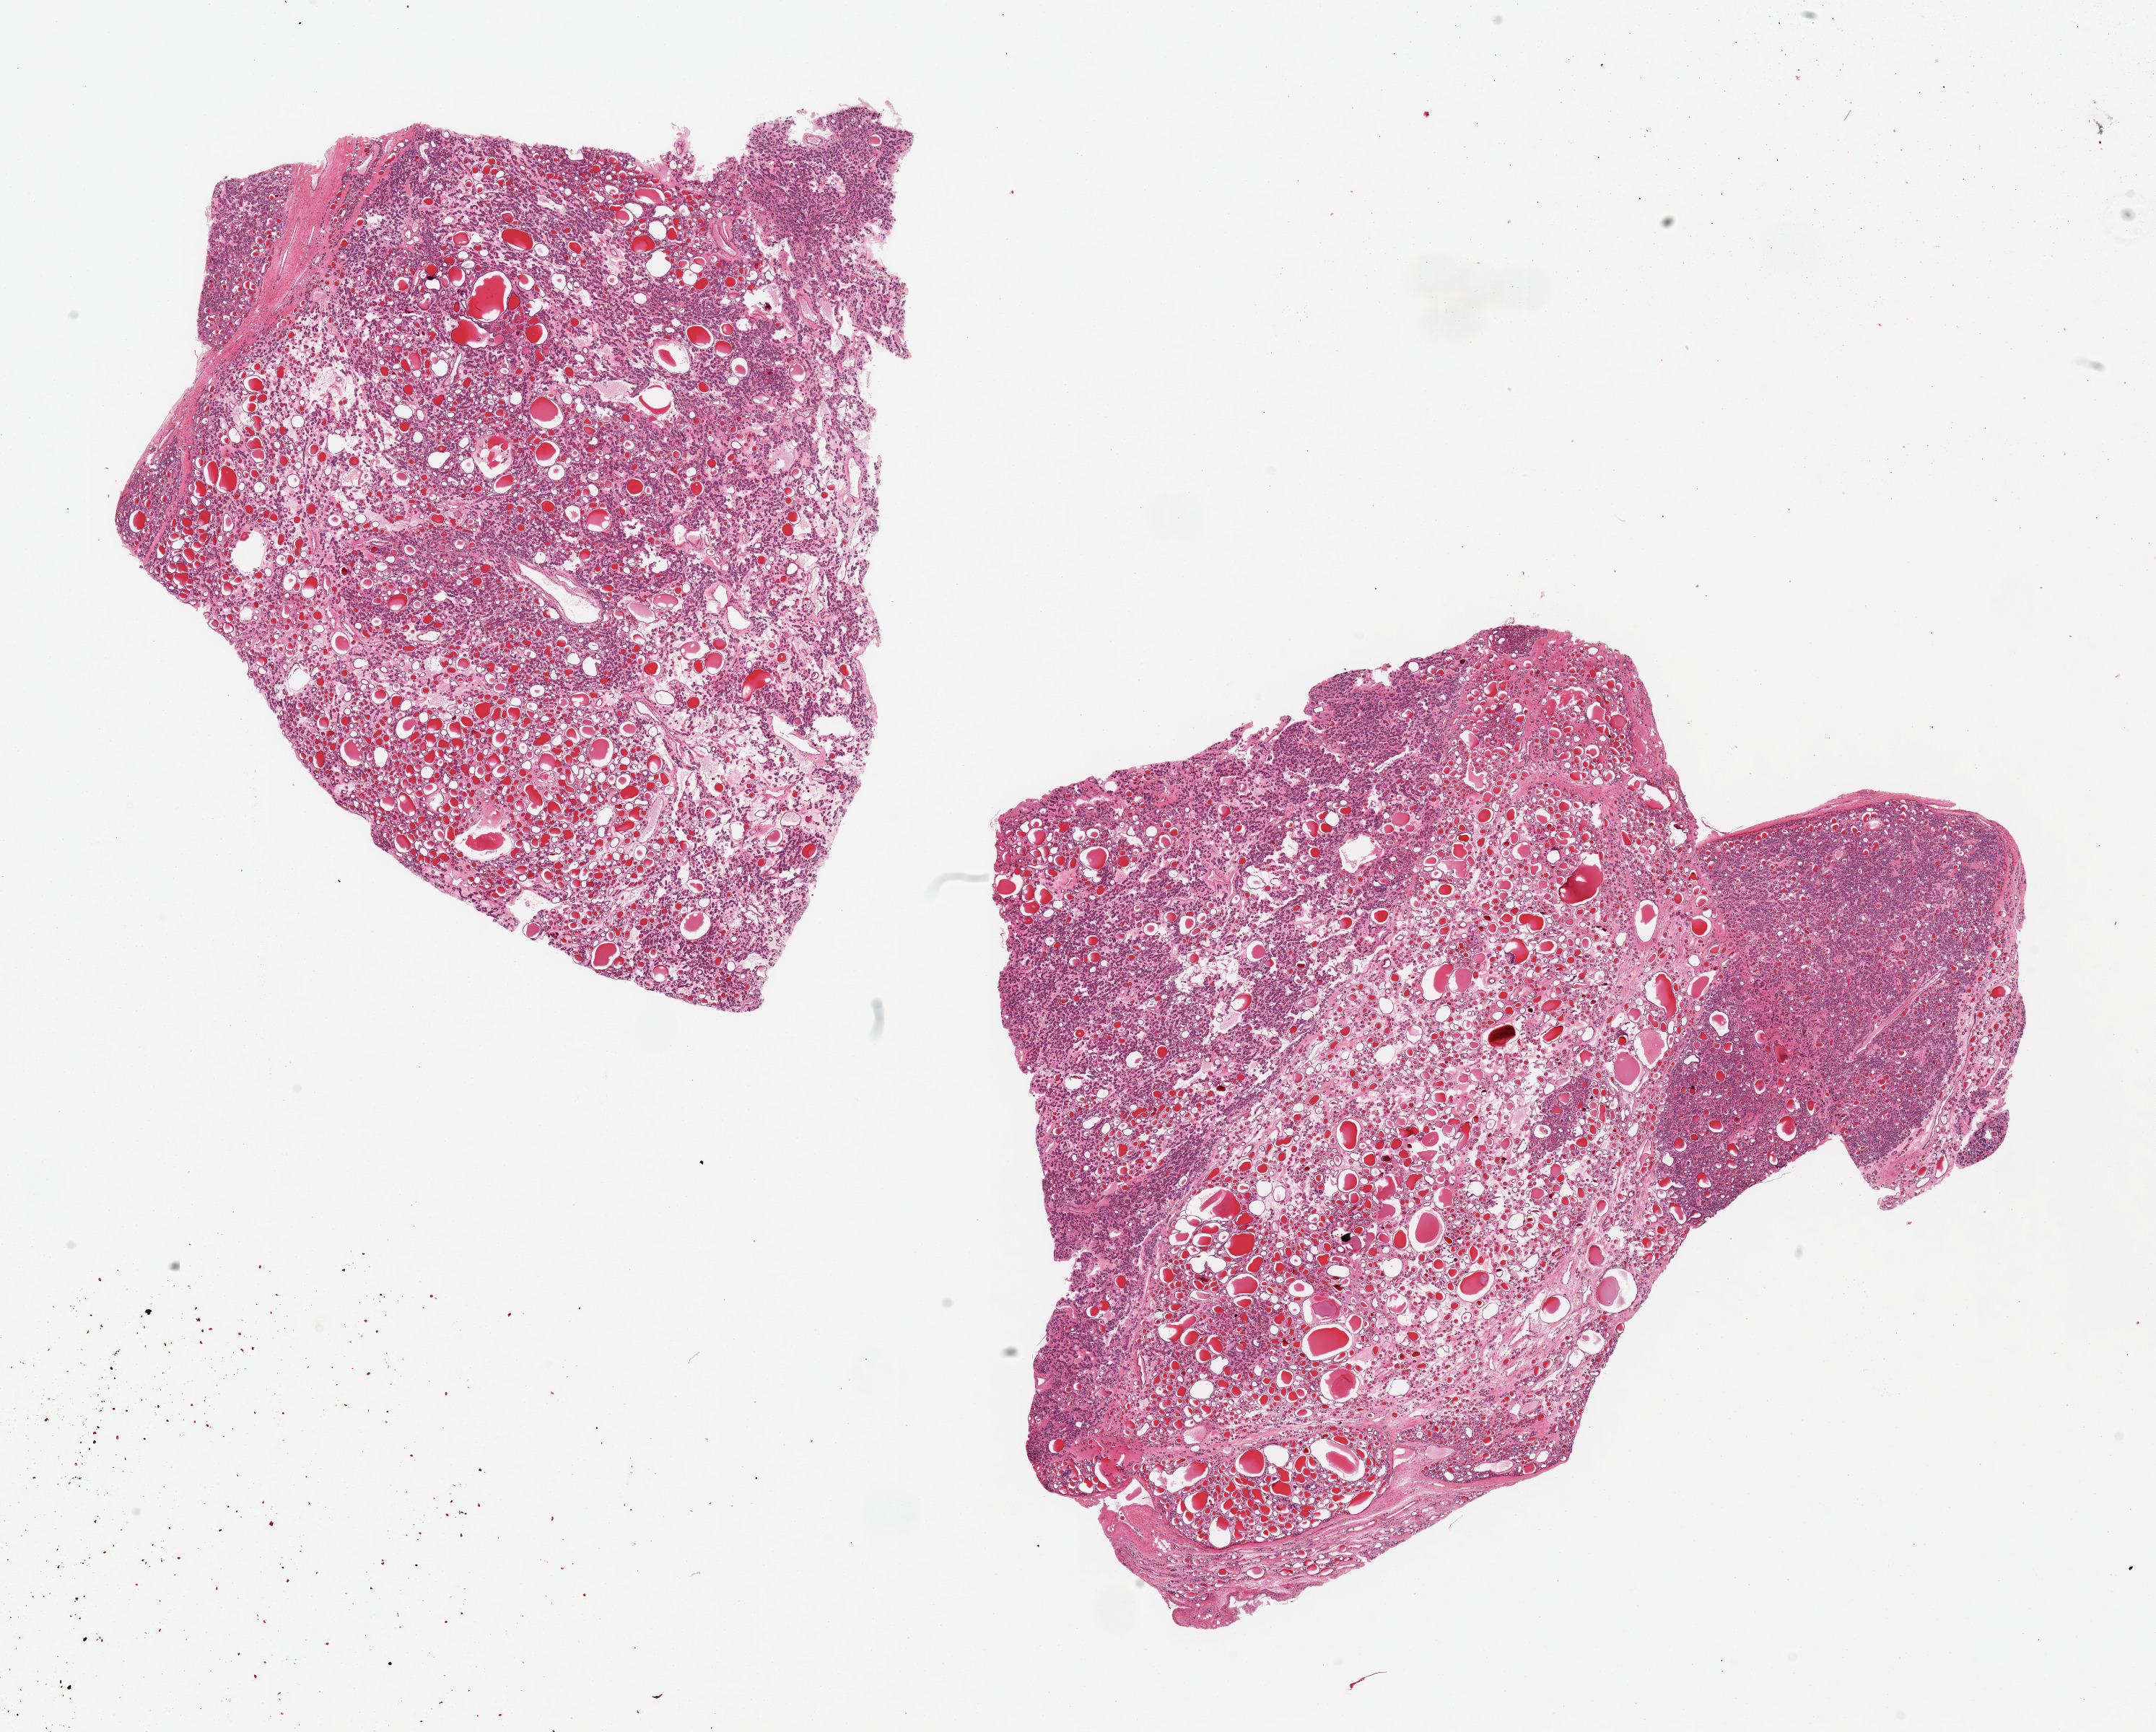
Whole-slide image, hematoxylin and eosin (H&E) stain — a low-resolution overview of the entire scanned area, about 23.6 x 19.0 mm, PAXgene-fixed paraffin-embedded (PFPE) section, section of thyroid (target tissue), donor tissue sample. Male donor.
• pathologist's review note for this sample: 2 pieces 11x9 & 10x7 mm; microfollicular adenomatoid nodules